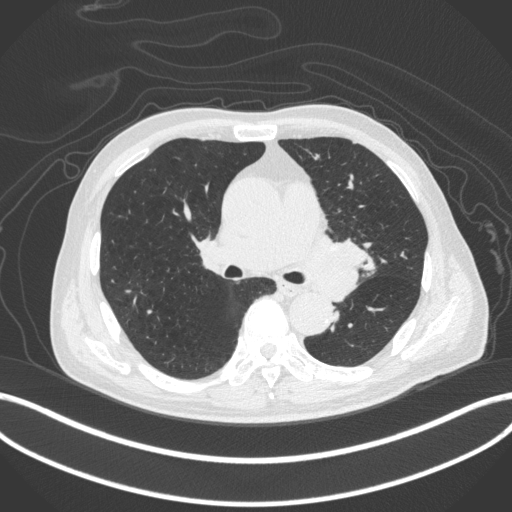
Chest CT, one axial slice; slice 256 of 420 in the series (ordered by position); reconstruction kernel B31f; 120 kVp; lung window (W 1500 / L -600 HU); 1 mm slice thickness; 512 × 512 image matrix, field of view 400 × 400 mm. Male patient, age 77 years. Case-level facts recorded for this patient, not image findings: clinical TNM (as recorded): T3 N1 M0.
Structures marked on this image (bounding box drawn by a radiologist):
- lung tumour (recorded histology: adenocarcinoma): box from (x=302, y=224) to (x=376, y=304) px